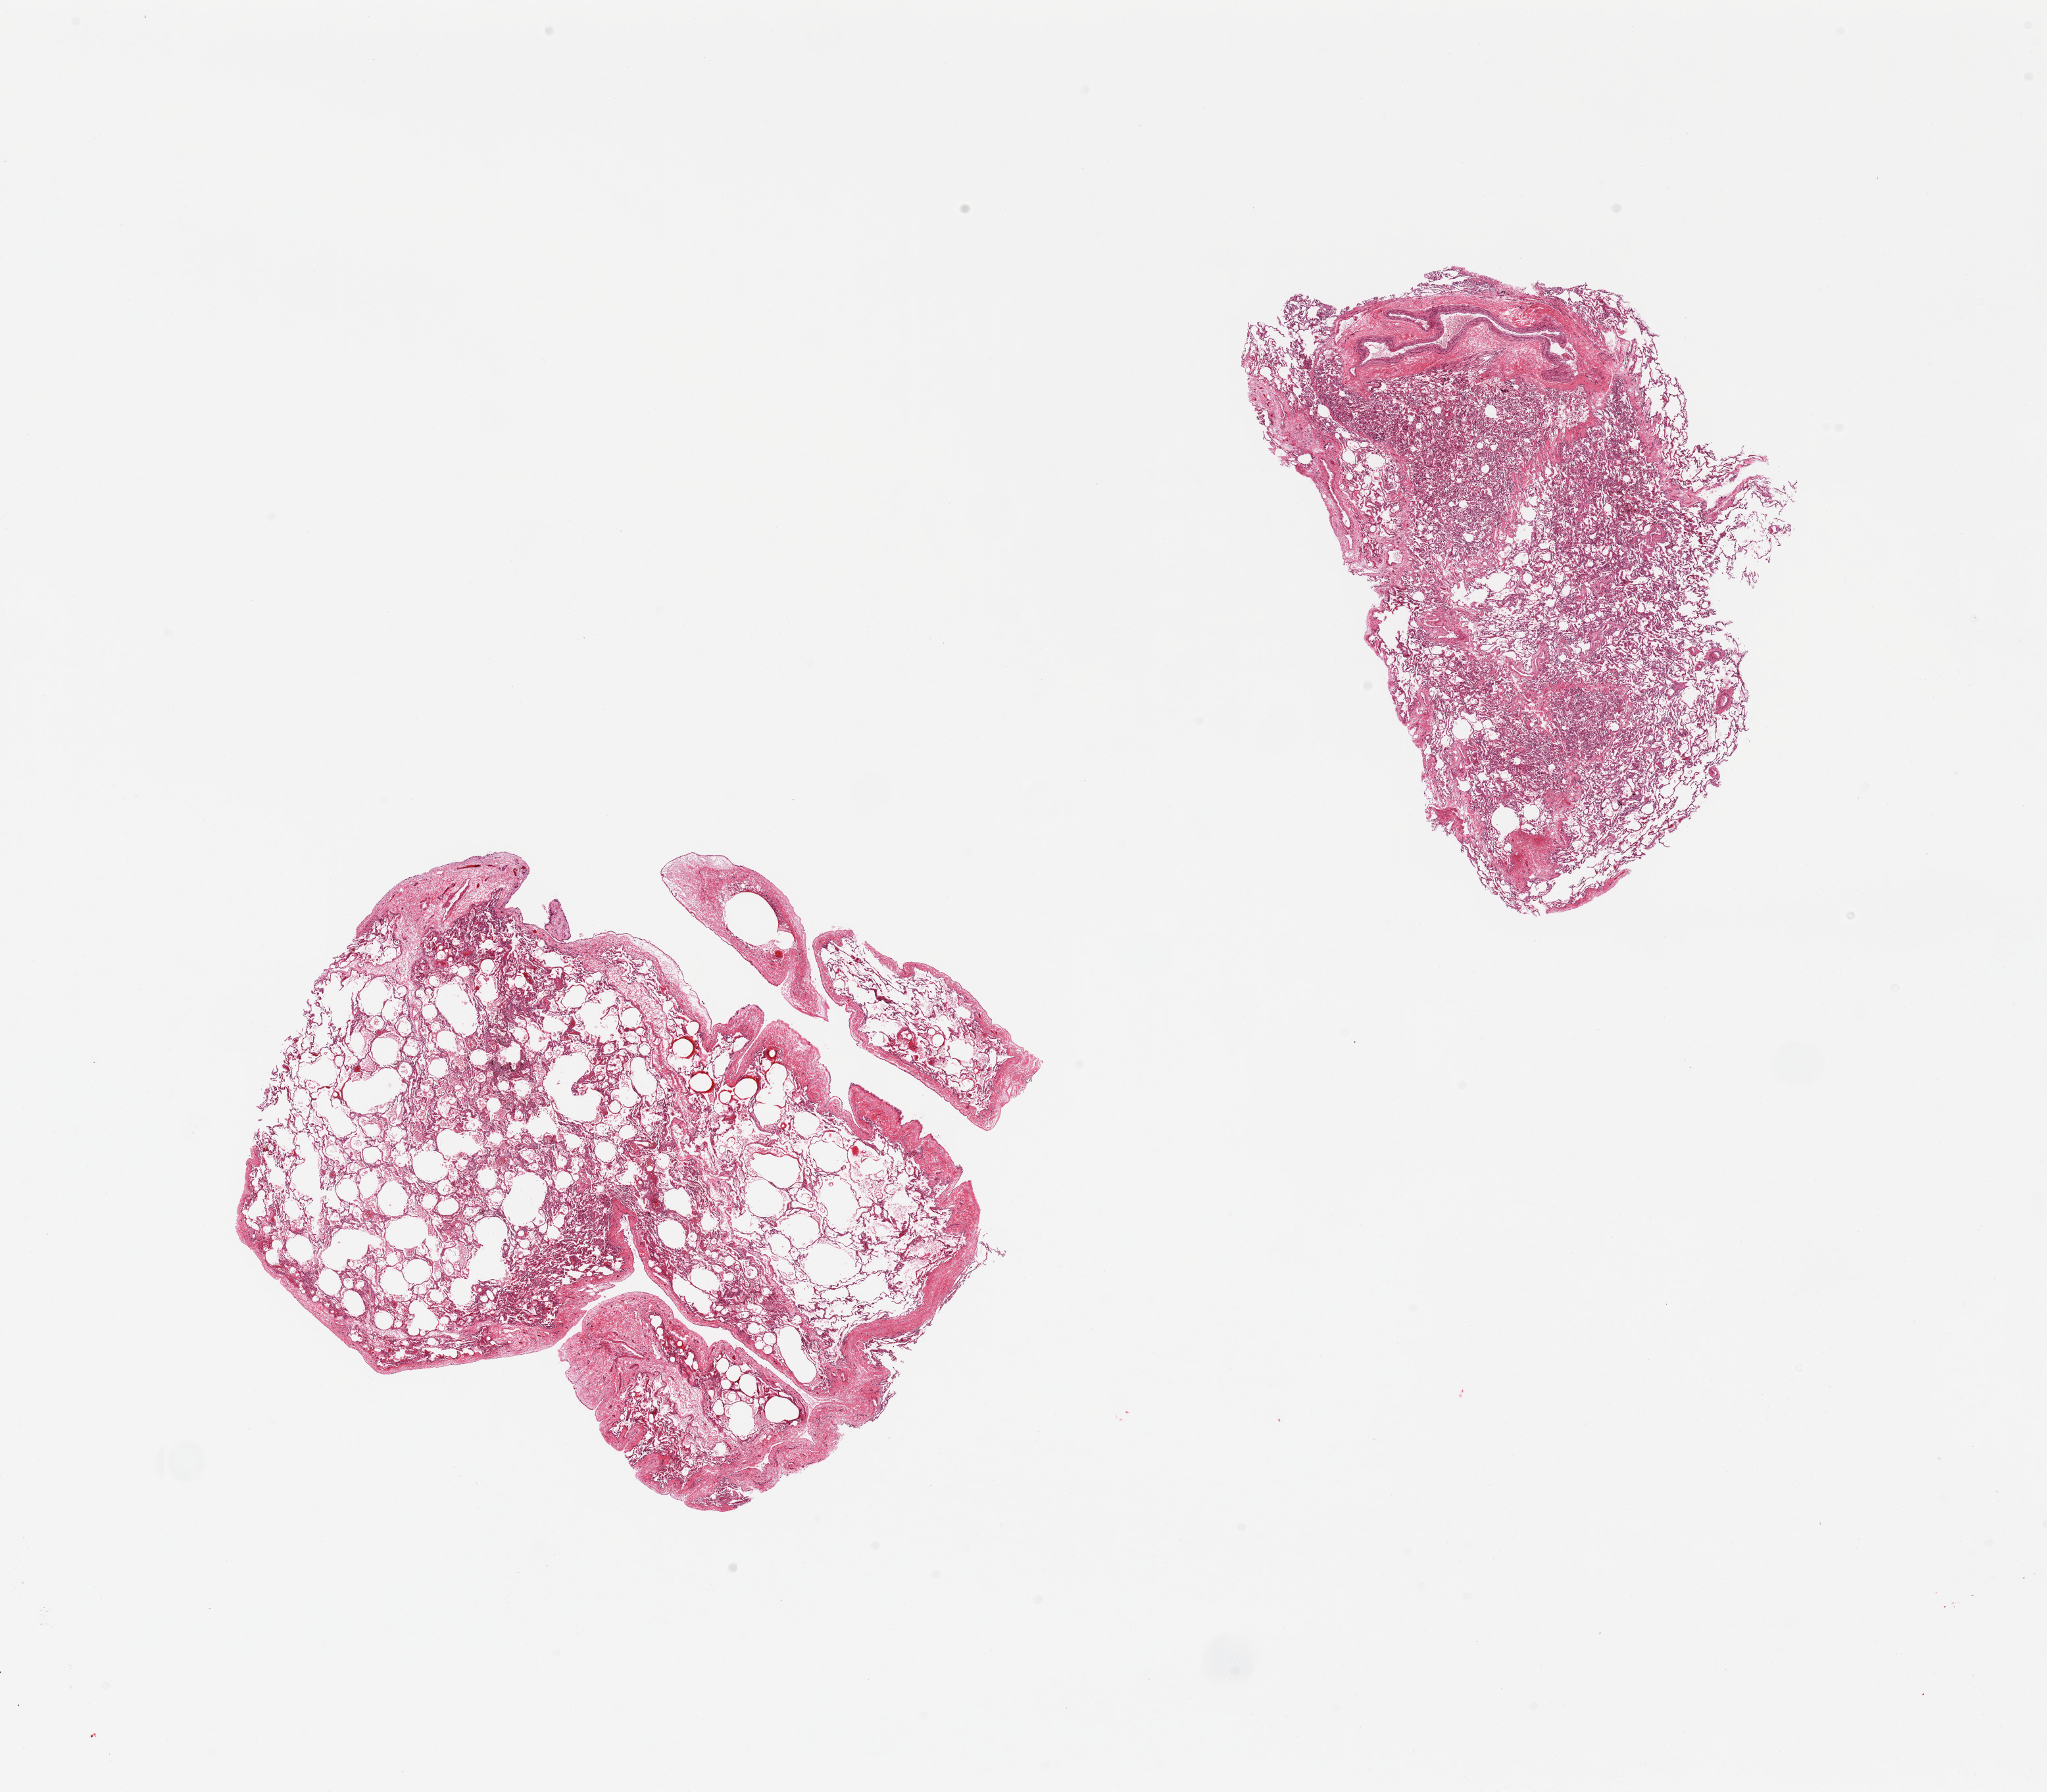
H&E whole-slide image, whole scanned area (about 24.6 x 21.6 mm, slide scanned at 20x) shown as a low-resolution overview, PAXgene-fixed, paraffin-embedded tissue, sampled site (target tissue): lung, tissue donor sample. Donor: male.
• pathologist's review note for this sample: 2 pieces, mild congestion